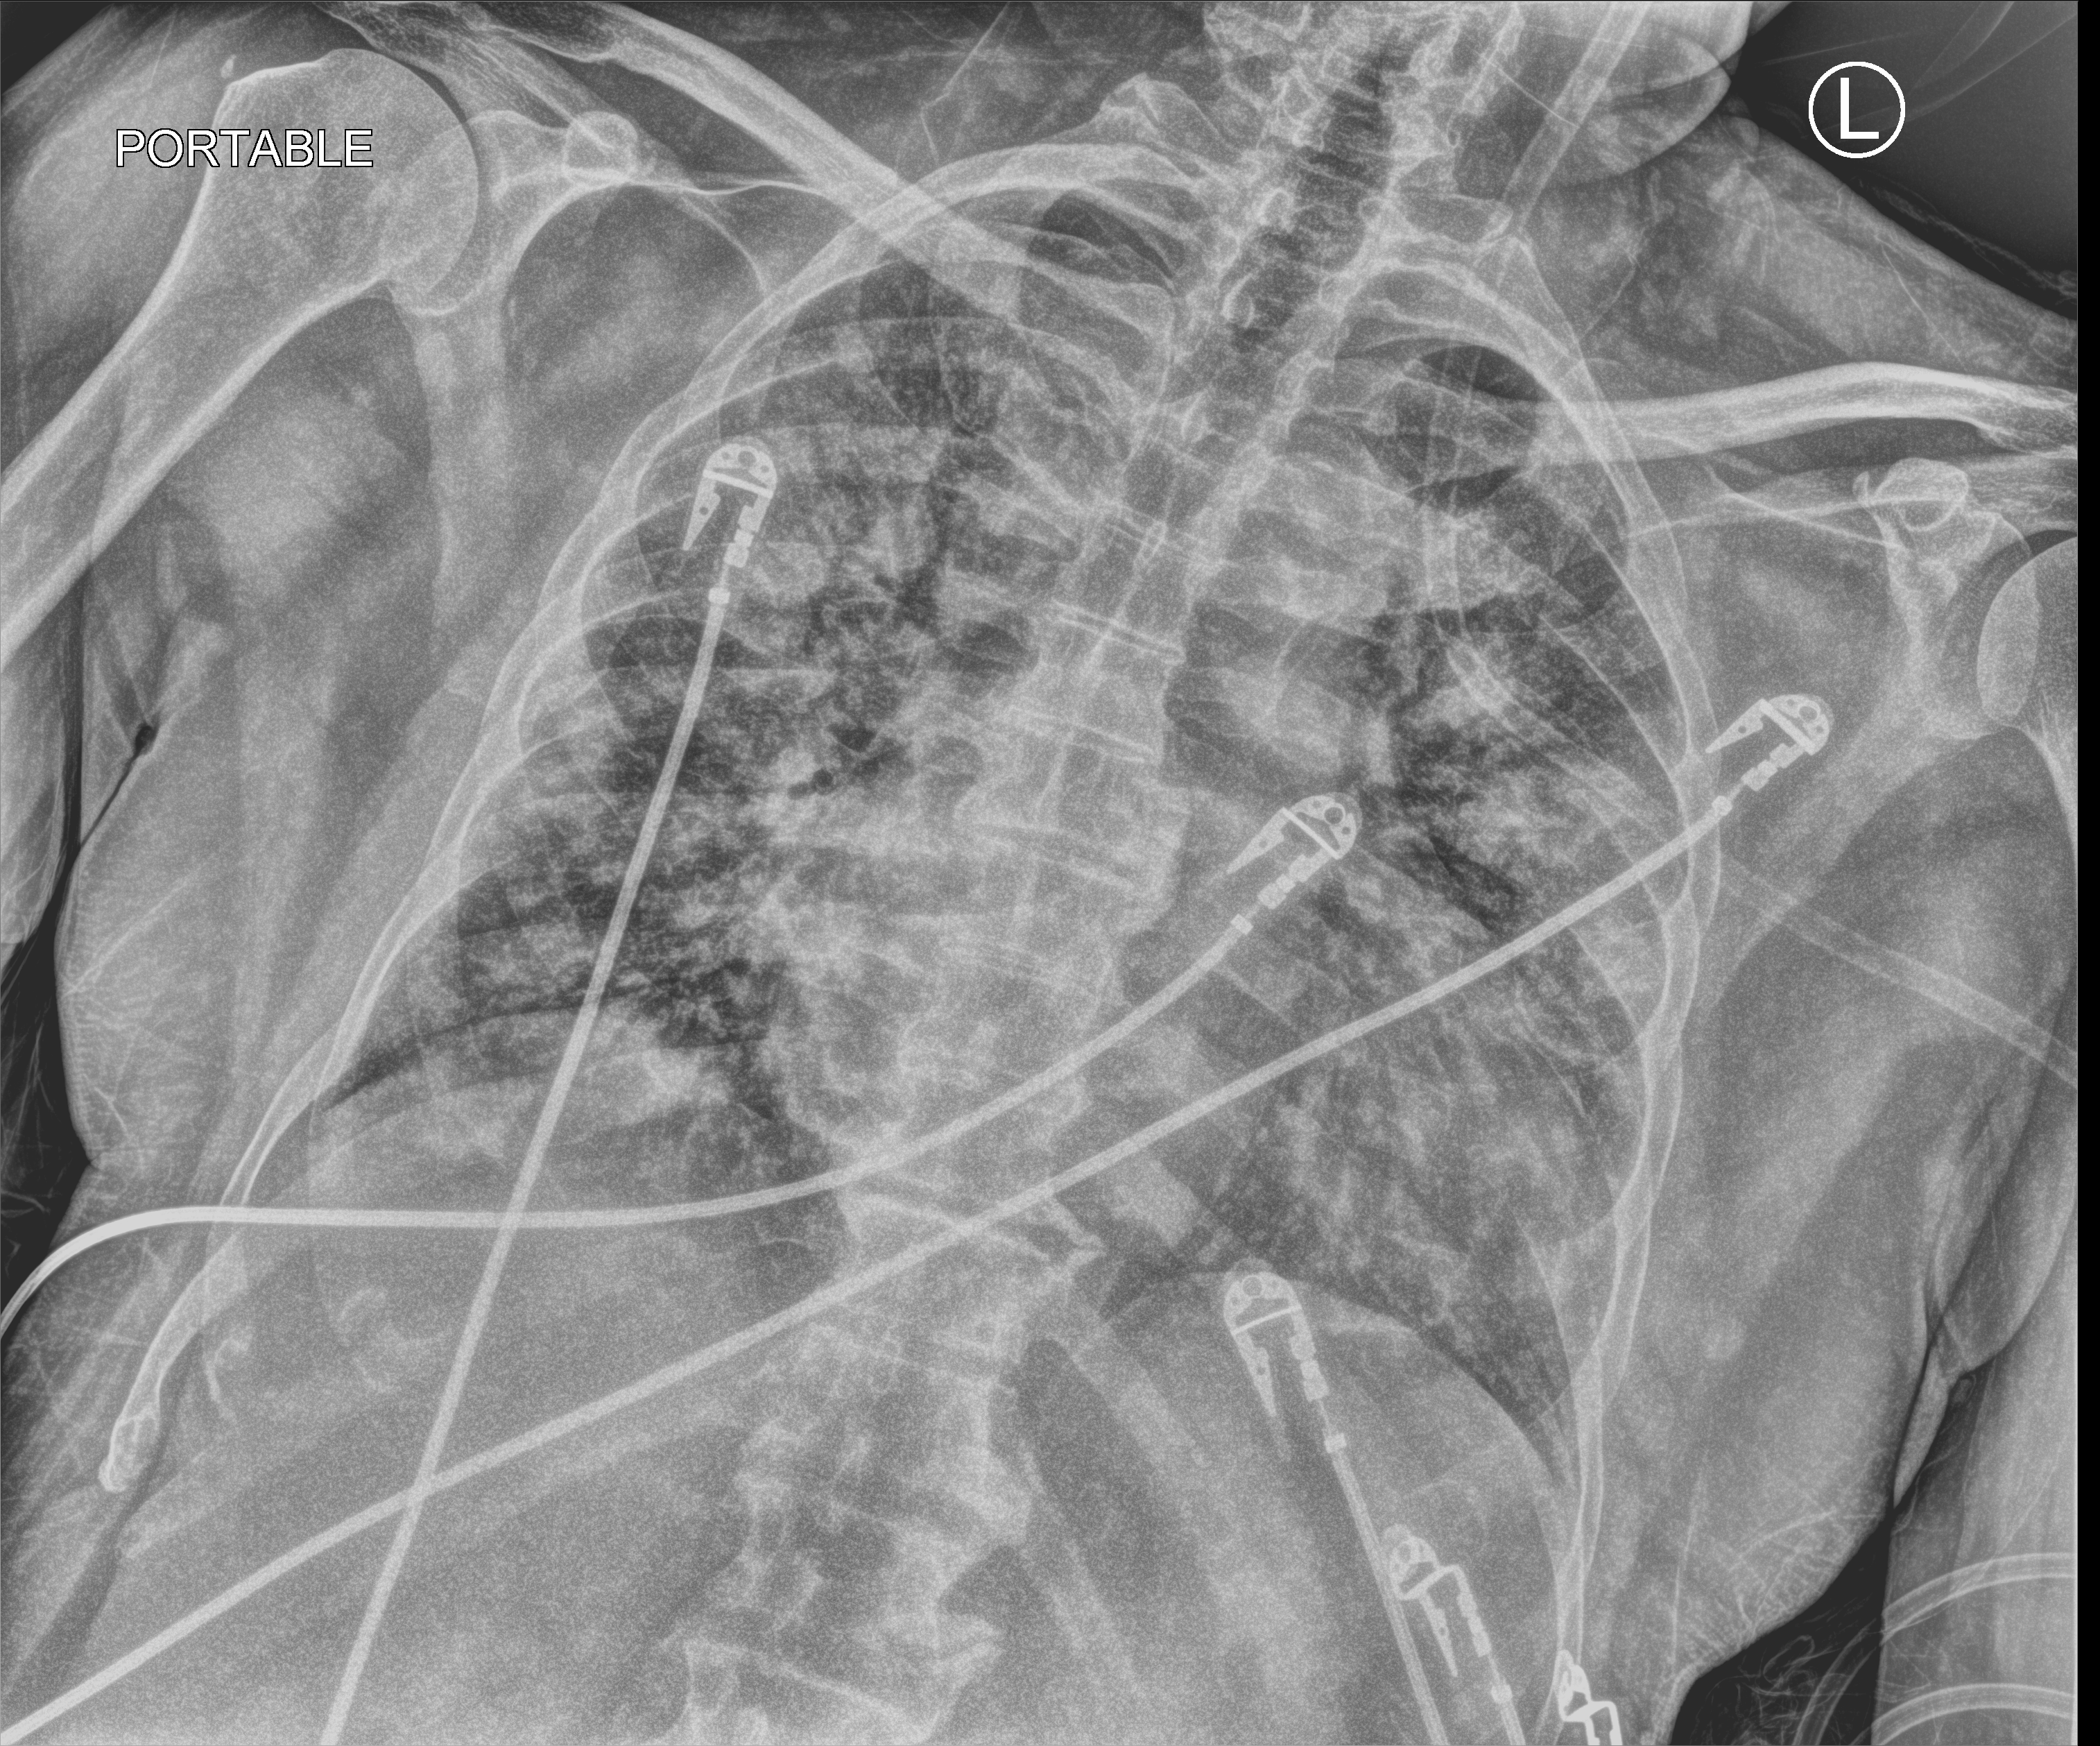
Chest X-ray (portable). Male patient hospitalised with COVID-19, age 60–74 years.
Admission-level facts for this patient (not findings on this image; timing relative to this image not recorded): admitted to intensive care during this hospital stay: yes.